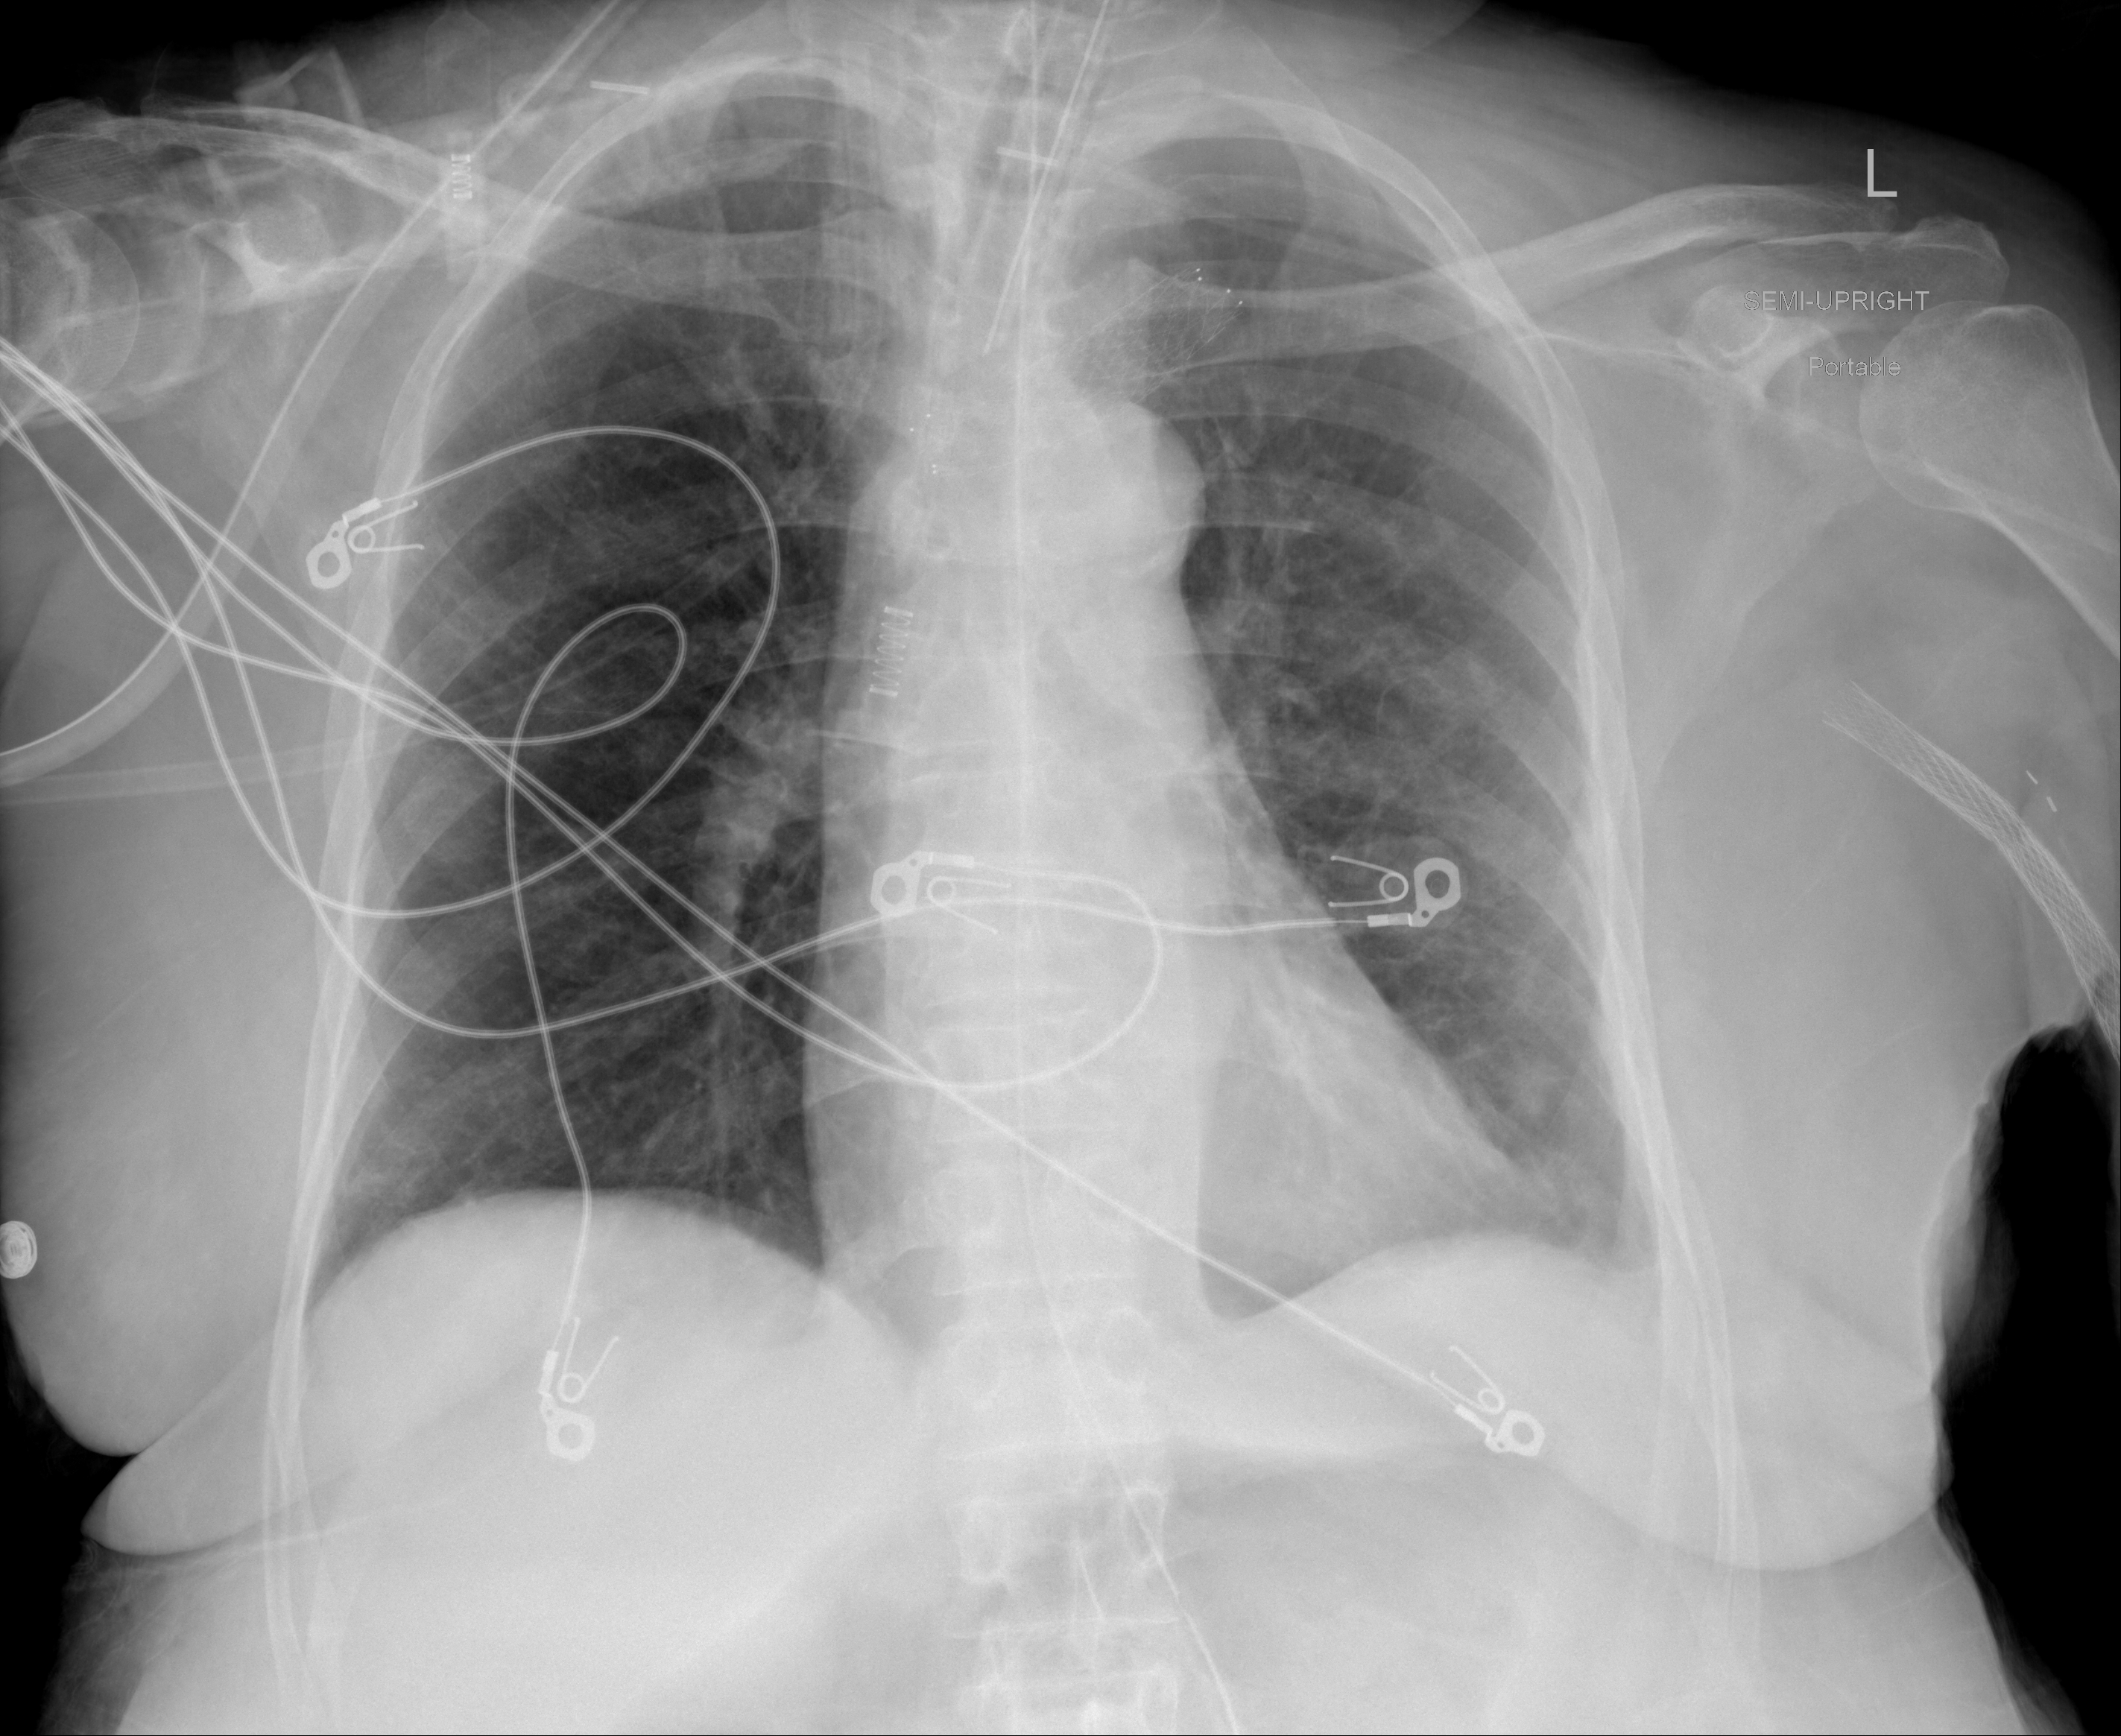
Chest X-ray (portable), AP projection. Female patient, age 64 years; imaged 18 days after the COVID-19 diagnosis.
Radiologist key findings (as recorded): marked improvement in previous bilateral airspace disease with minimal residual at left base, right lung now essentially clear.